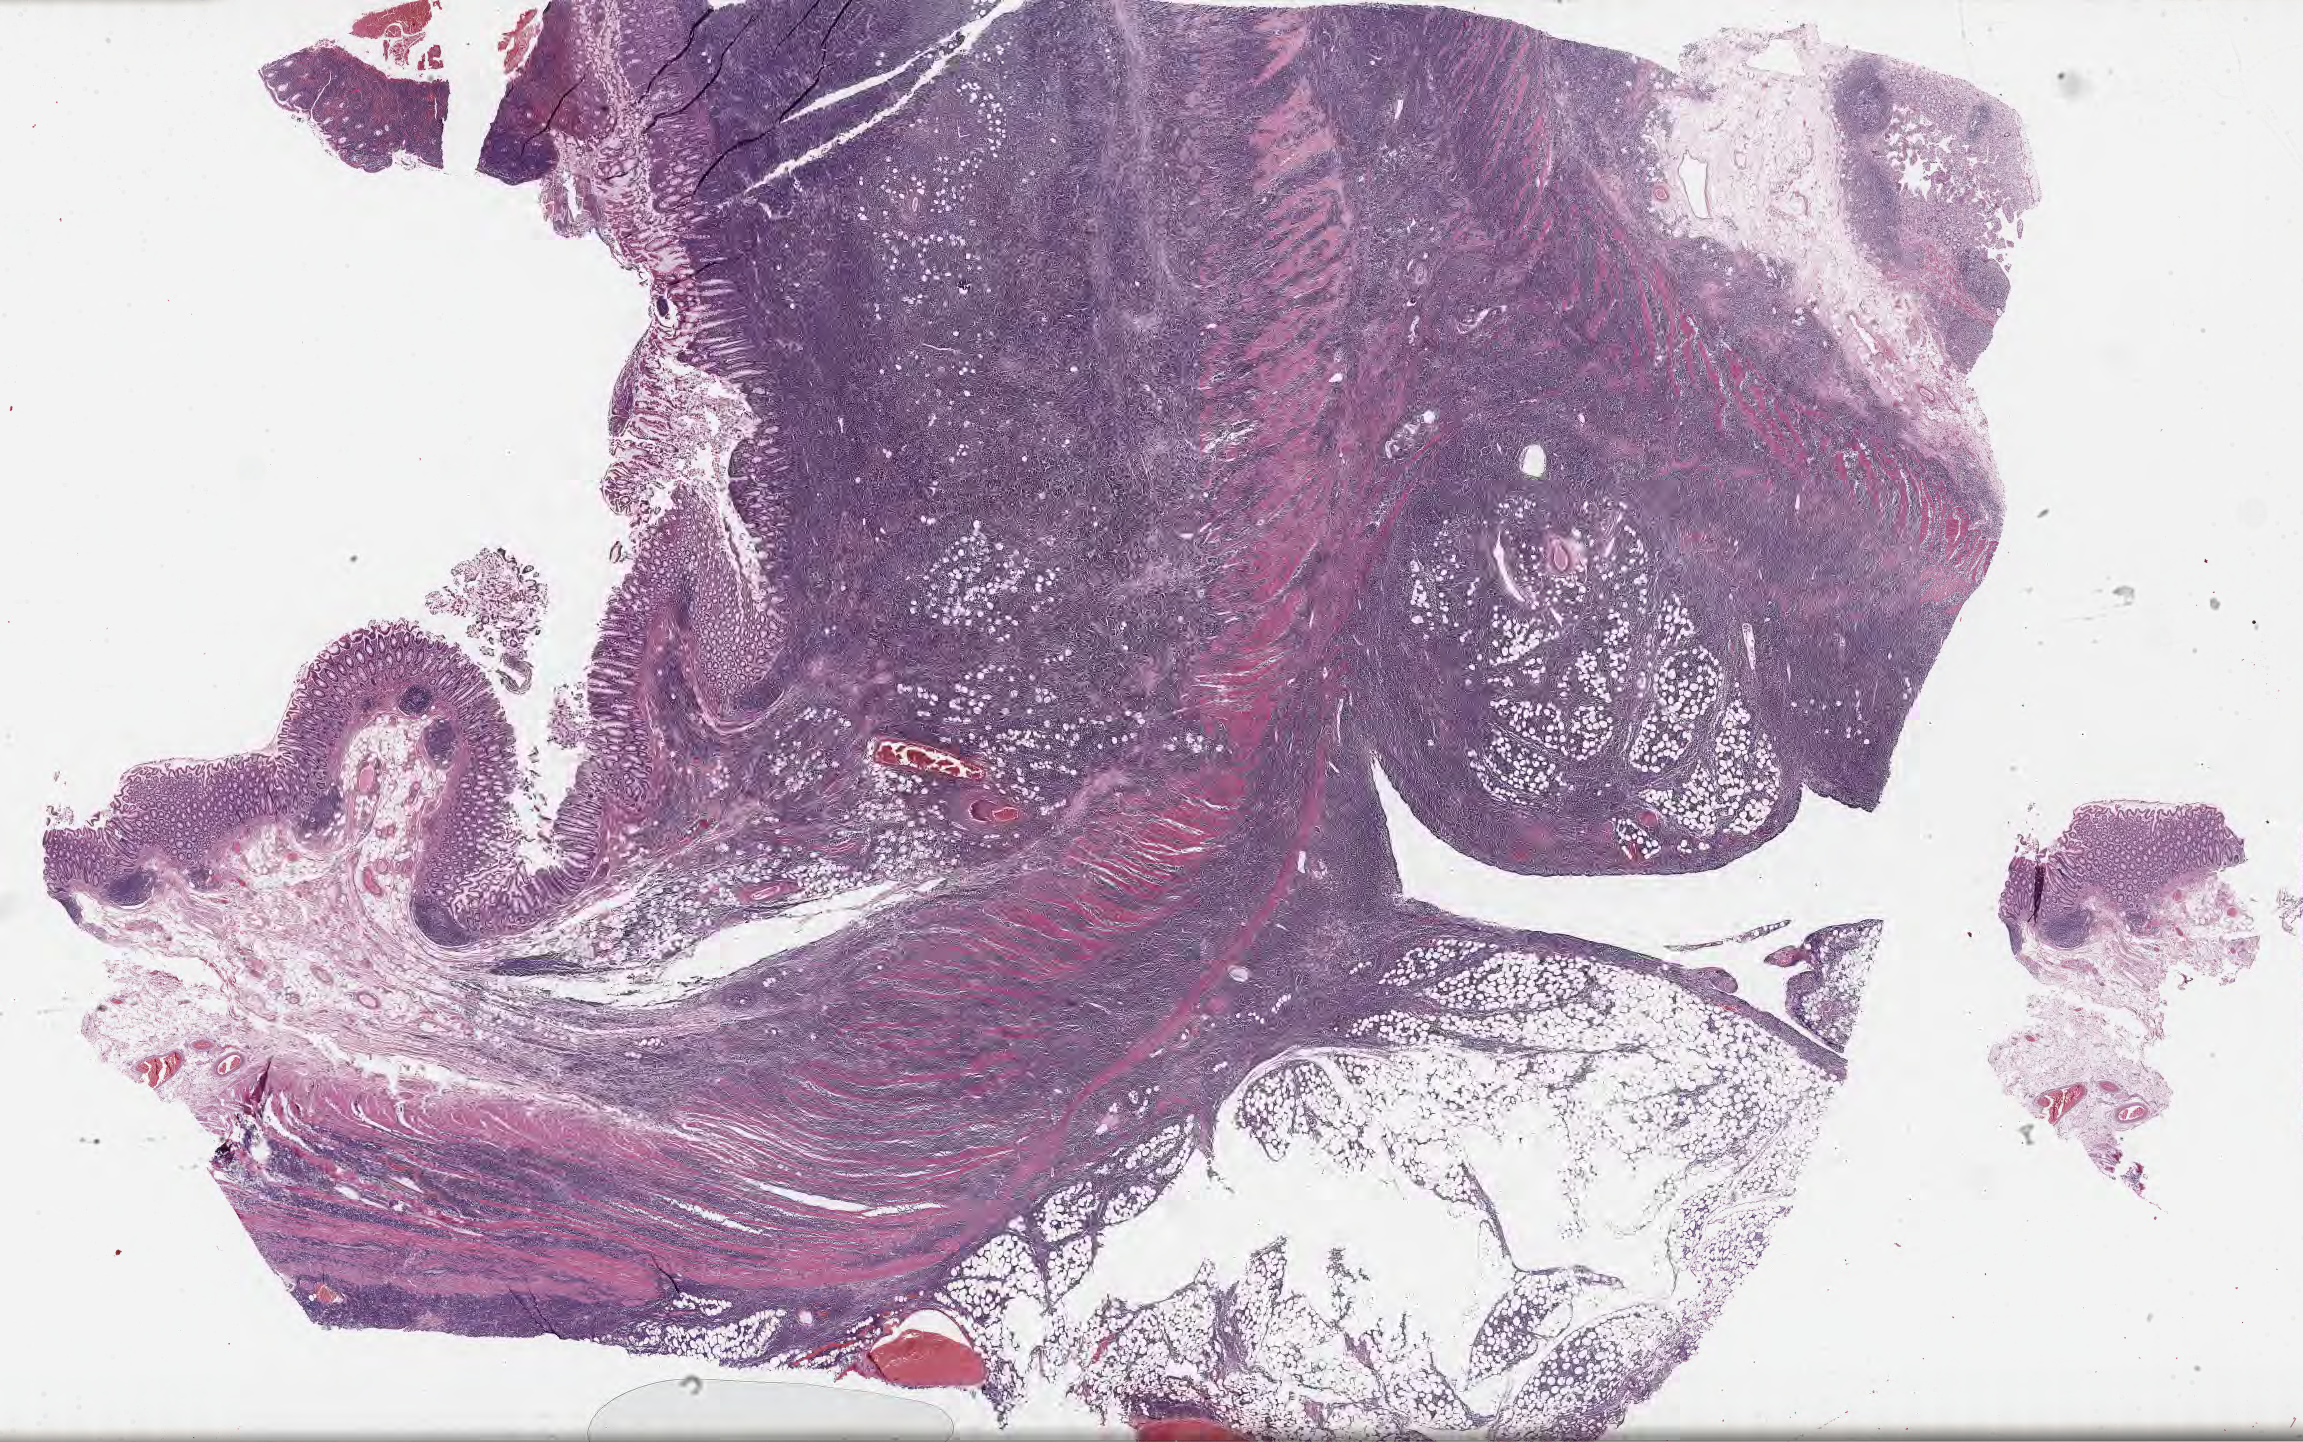
Whole-slide image, H&E stain — whole scanned area (about 37.2 x 23.3 mm) shown as a low-resolution overview; tumor tissue. Male patient, aged 56.
- histologic diagnosis: Burkitt lymphoma, NOS